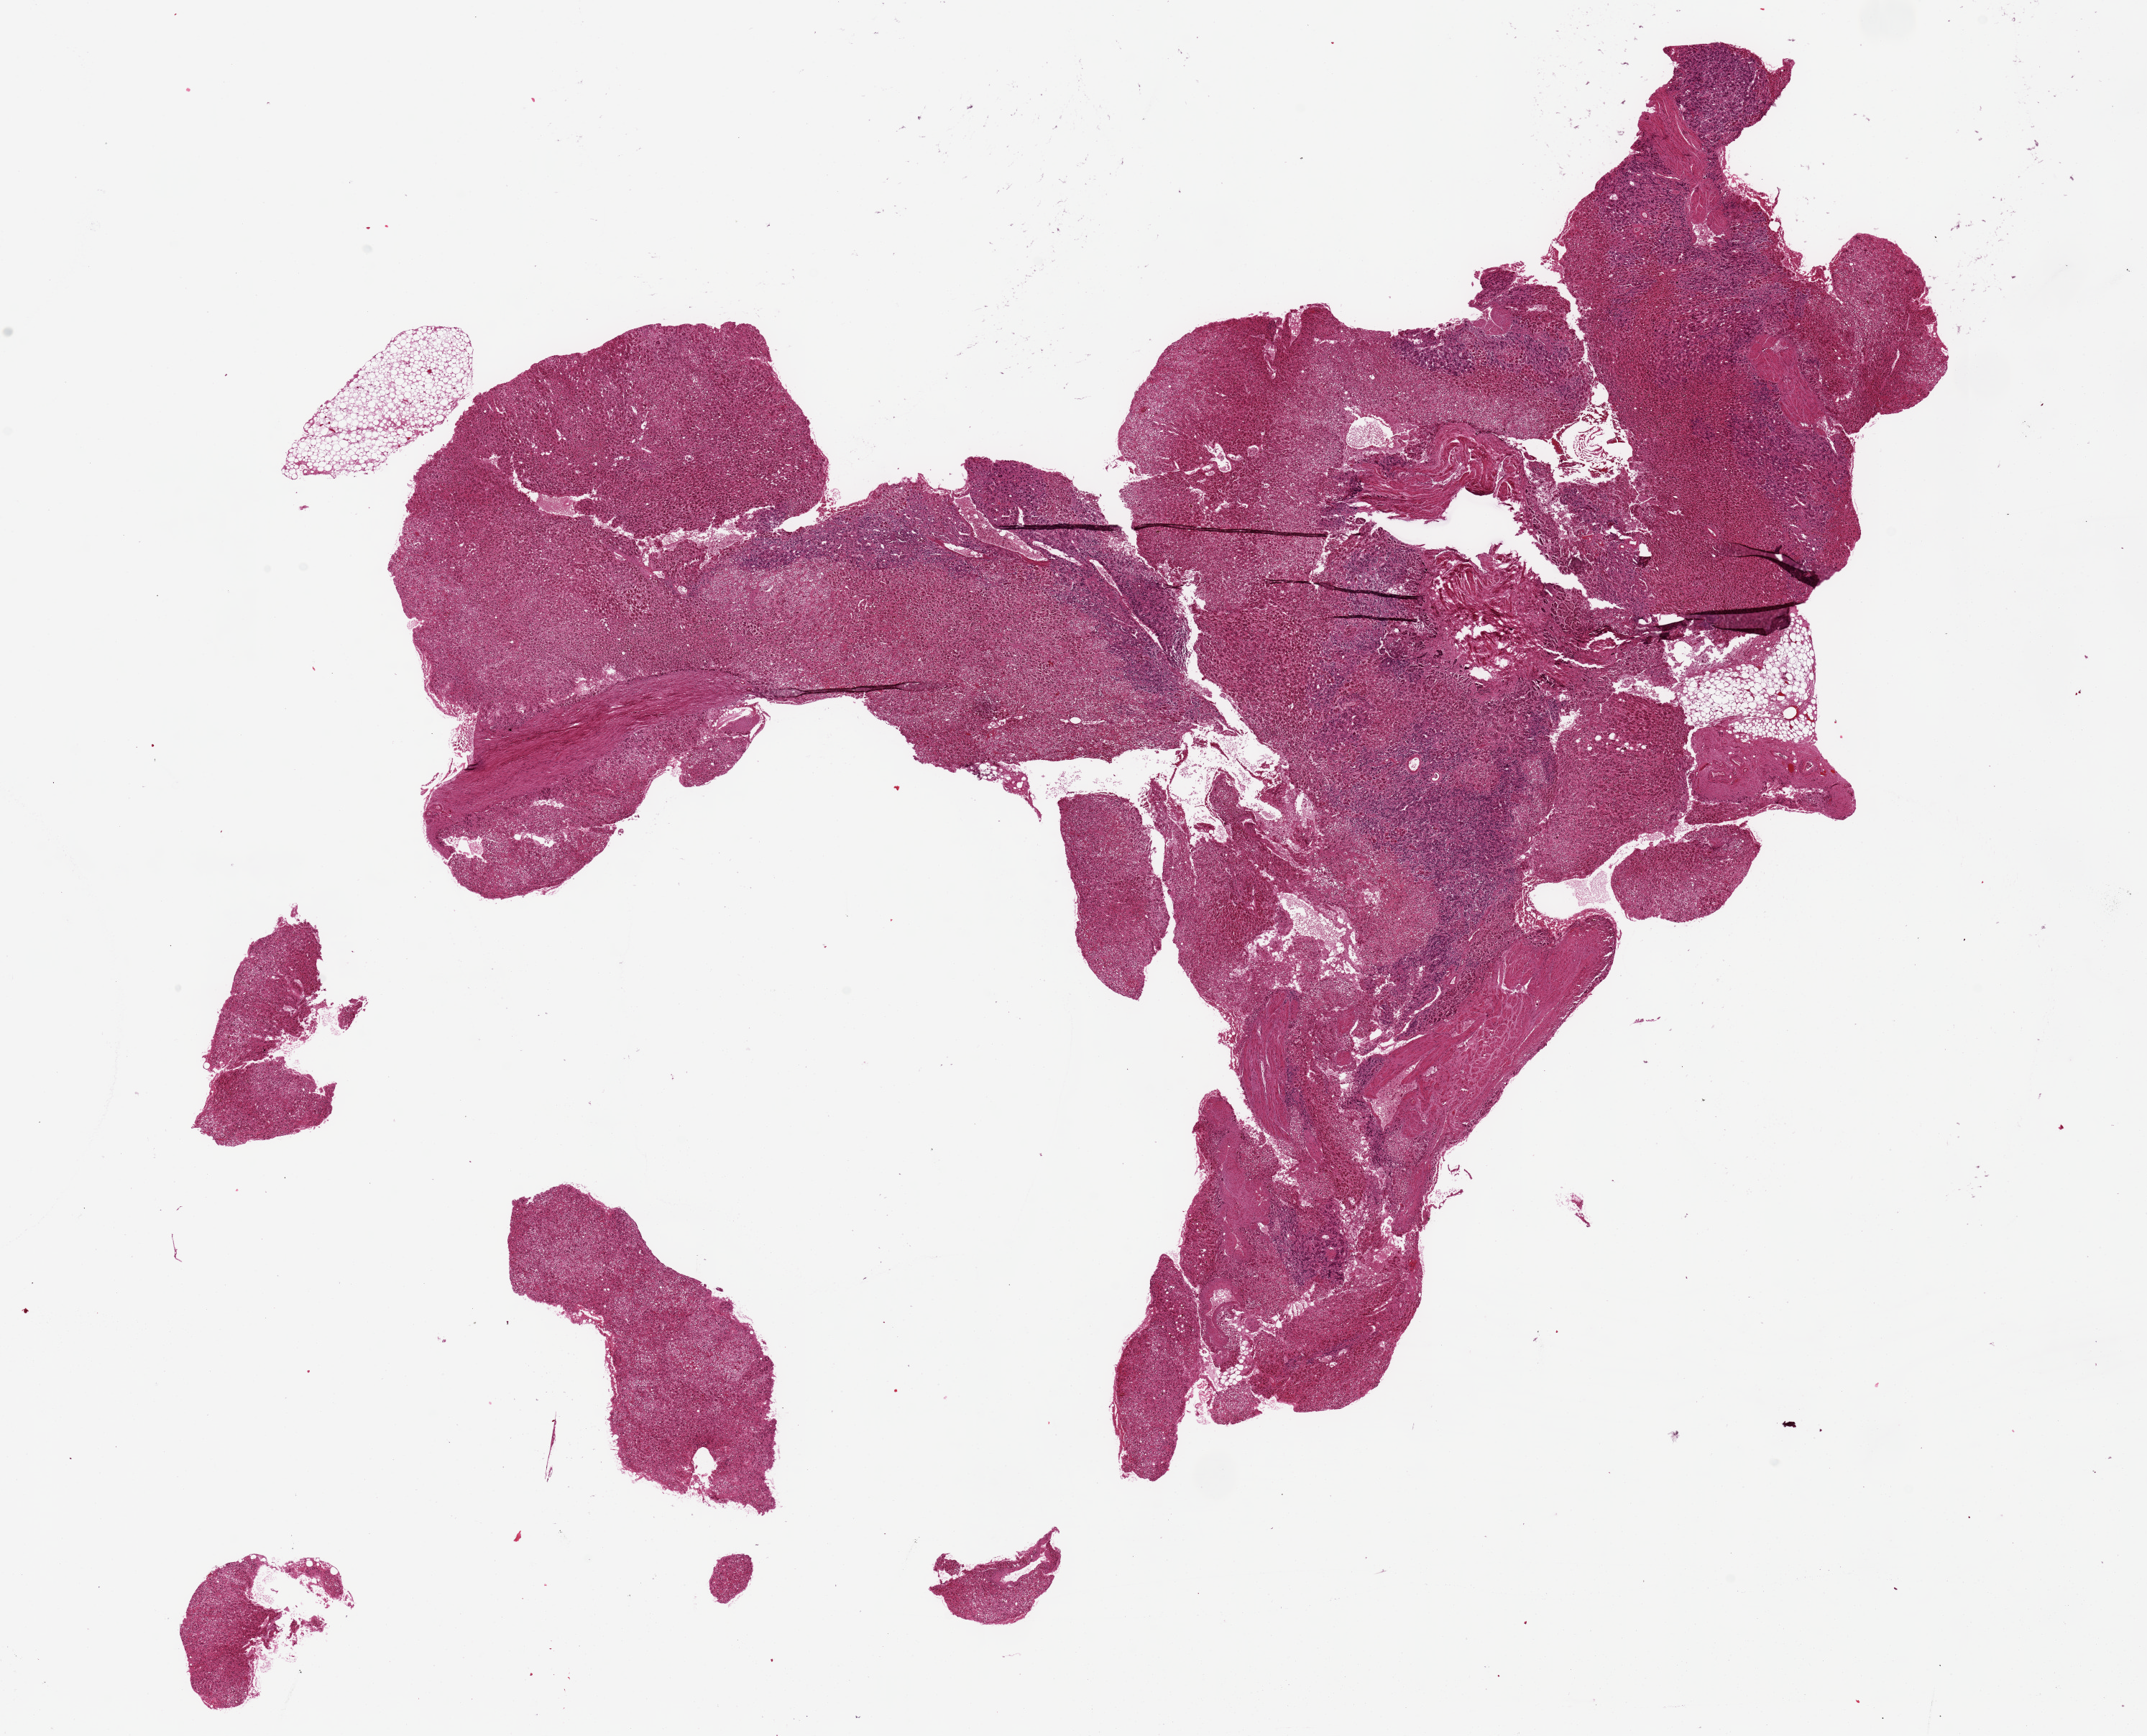
Digitized haematoxylin and eosin-stained section — a low-resolution overview of the entire scanned area, about 23.6 x 19.1 mm (acquisition: 20x scan). PAXgene-fixed, paraffin-embedded tissue. Target tissue: adrenal gland. Donor tissue sample. Donor sex: female.
Pathologist's review note for this sample: Moderate autolysis (???score 2???)???cortex is 90+% of specimen.